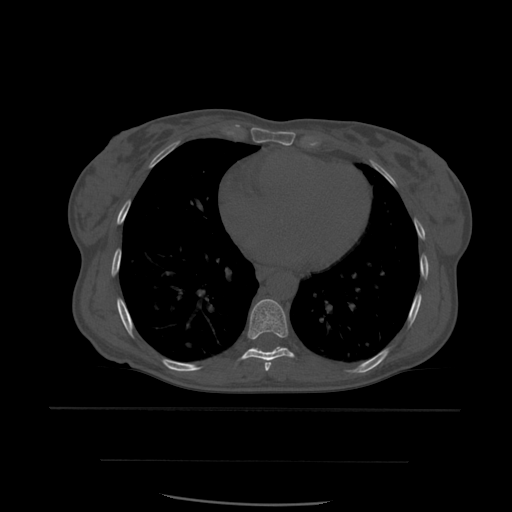
CT including the spine, one axial slice. Slice 355 of 574 in the series (ordered by position). Bone window (W 1800 / L 400 HU). 1.25 mm slice thickness. 512 × 512 image matrix. Patient age 48 years. From the clinical record (not read from this slice): primary cancer: lung; vertebrae with lytic lesions (as recorded): T11.
Outlined on this slice (semi-automatically segmented with operator editing):
- T7 vertebra: bounding box (x1, y1, x2, y2) in pixels: (265, 363, 271, 371)
- T8 vertebra: (240, 299, 296, 371)
- T9 vertebra: (251, 347, 258, 350)